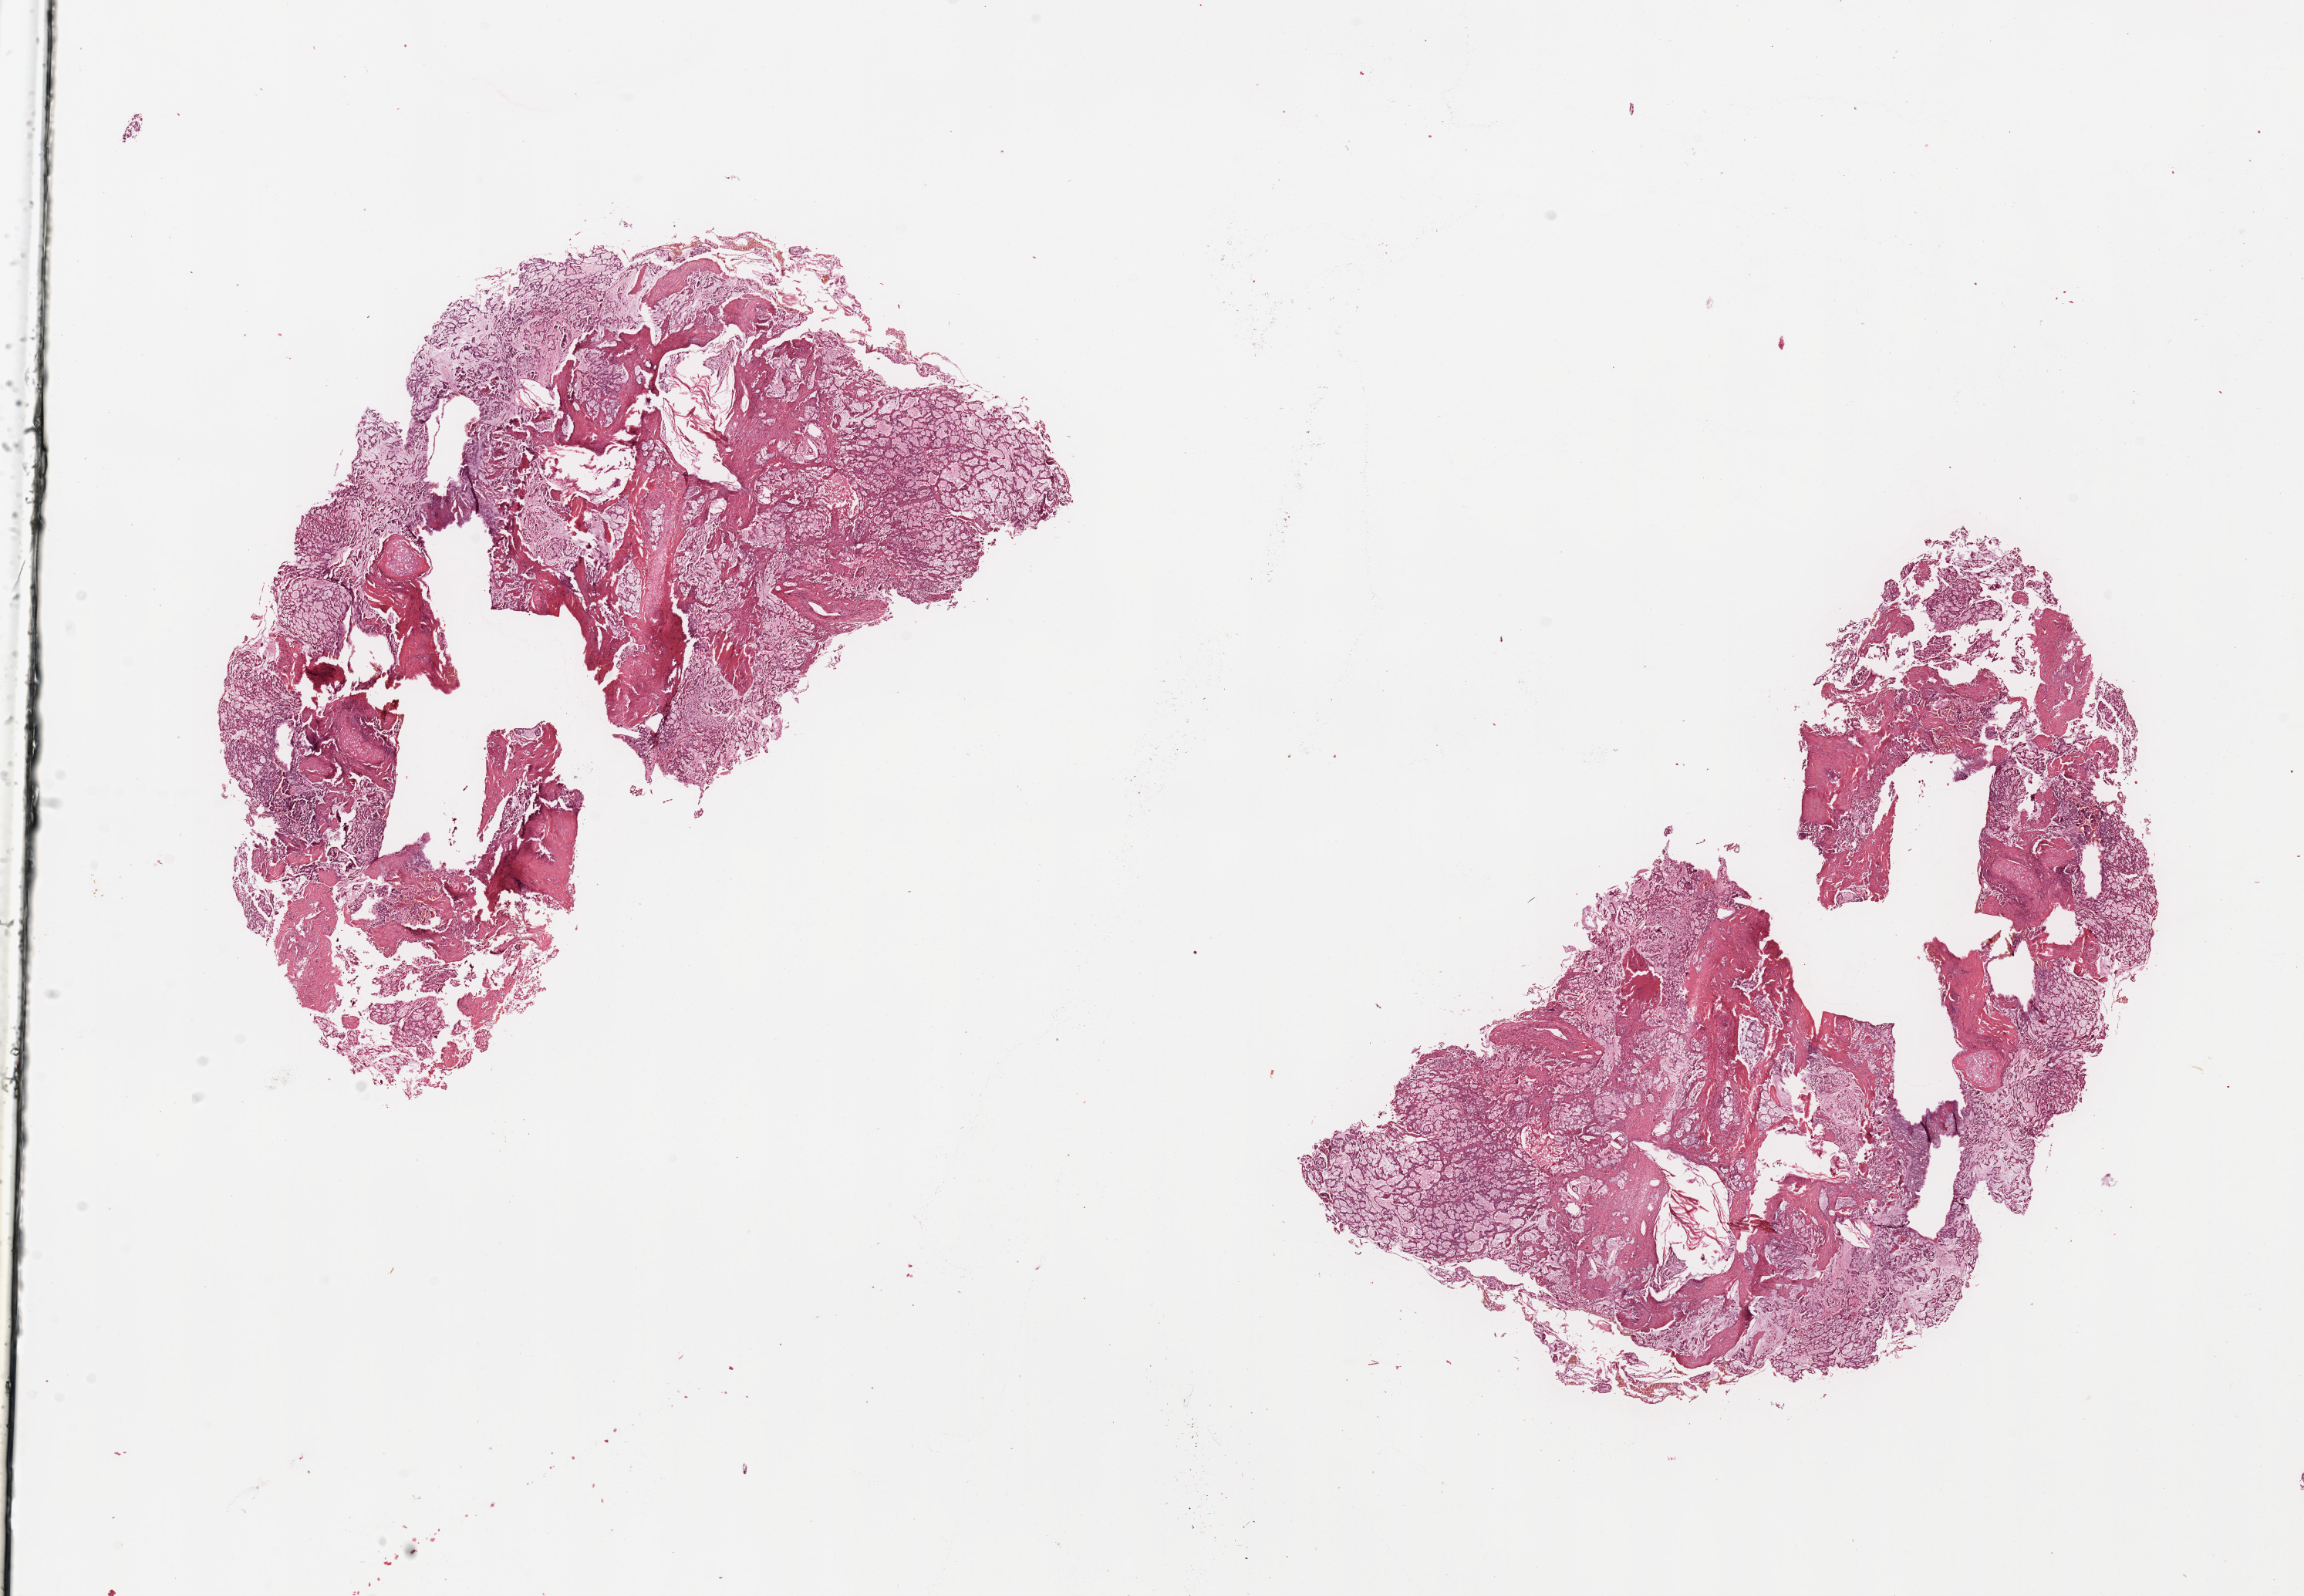
Digitized H&E-stained tissue section (whole slide), low-resolution overview of the scanned area, about 23.6 x 16.4 mm (acquisition: 20x scan), tumour tissue sample, lung. Patient: female, age 36 years. Histologic grade: G2 (moderately differentiated).
- AJCC pathologic stage: IIIA
- diagnosis: Adenocarcinoma, NOS
- primary tumour site (as recorded): left upper lobe